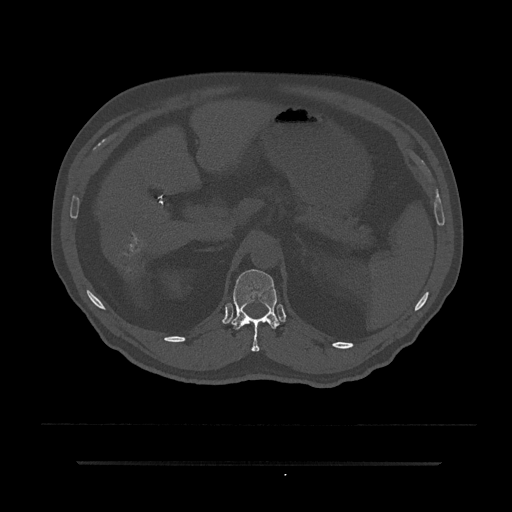
CT including the spine, one axial slice; slice 214 of 797 in the series (ordered by position); reconstruction kernel Br40s/3; bone window (W 1800 / L 400 HU); 512 × 512 image matrix, field of view 464 × 464 mm. Male patient, age 59 years. From the clinical record (not read from this slice): primary cancer: bile ducts.
Outlined on this slice (semi-automatic segmentation, software-assisted and operator-edited):
- T12 vertebra: bounding box <232,269,279,352> (left, top, right, bottom; pixels)